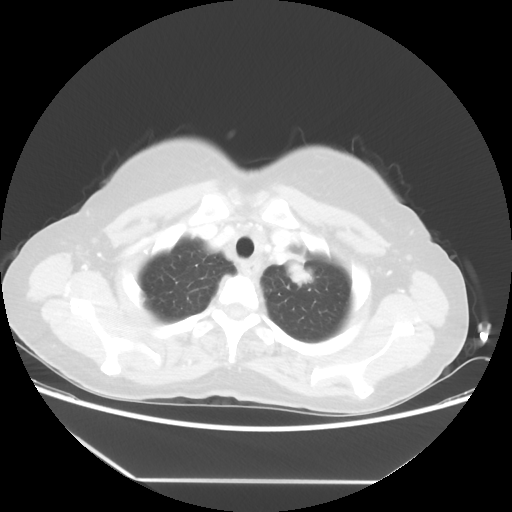
Chest CT, one axial slice. Slice 46 of 52 in the series (ordered by position). Reconstruction kernel STANDARD. 100 kVp. Lung window (W 1500 / L -600 HU). 5 mm slice thickness. 512 × 512 image matrix, field of view 390 × 390 mm. Female patient, age 50 years. From the clinical record (not read from this slice): clinical TNM (as recorded): T2 N3 M0.
Annotated regions visible in this slice (bounding box drawn by a radiologist):
- lung tumour (recorded histology: adenocarcinoma): bounding box <269,246,320,297> (left, top, right, bottom; pixels)